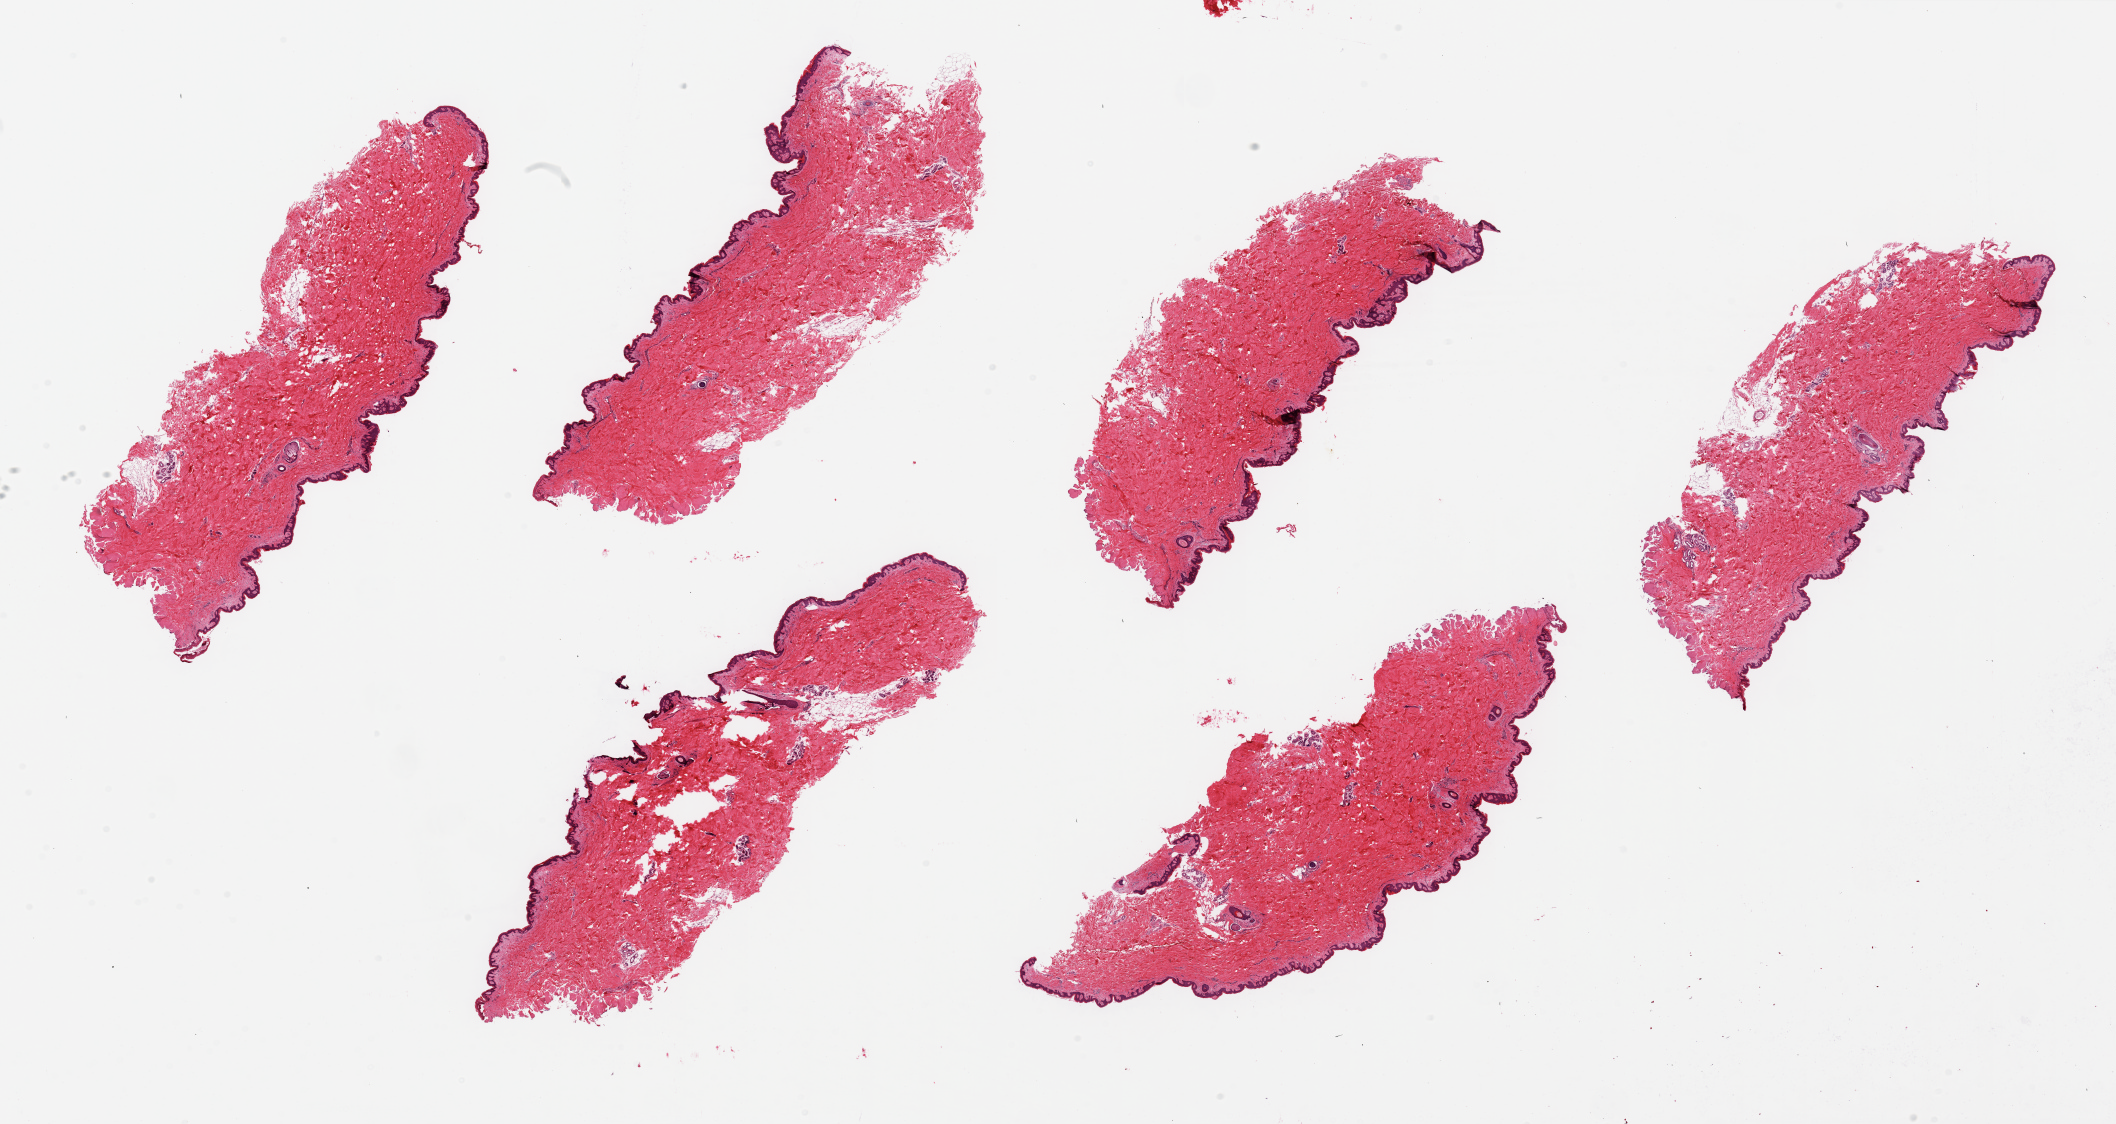
H&E whole-slide image, a low-resolution overview of the entire scanned area, about 33.5 x 17.8 mm (slide scanned at 20x), PAXgene-fixed, paraffin-embedded tissue, target tissue: skin of suprapubic region, tissue donor sample. Donor: male.
- reviewer comment on this tissue sample: 6 pieces, up to 10x4mm; squamous epithelium is ~1-2% of thickness